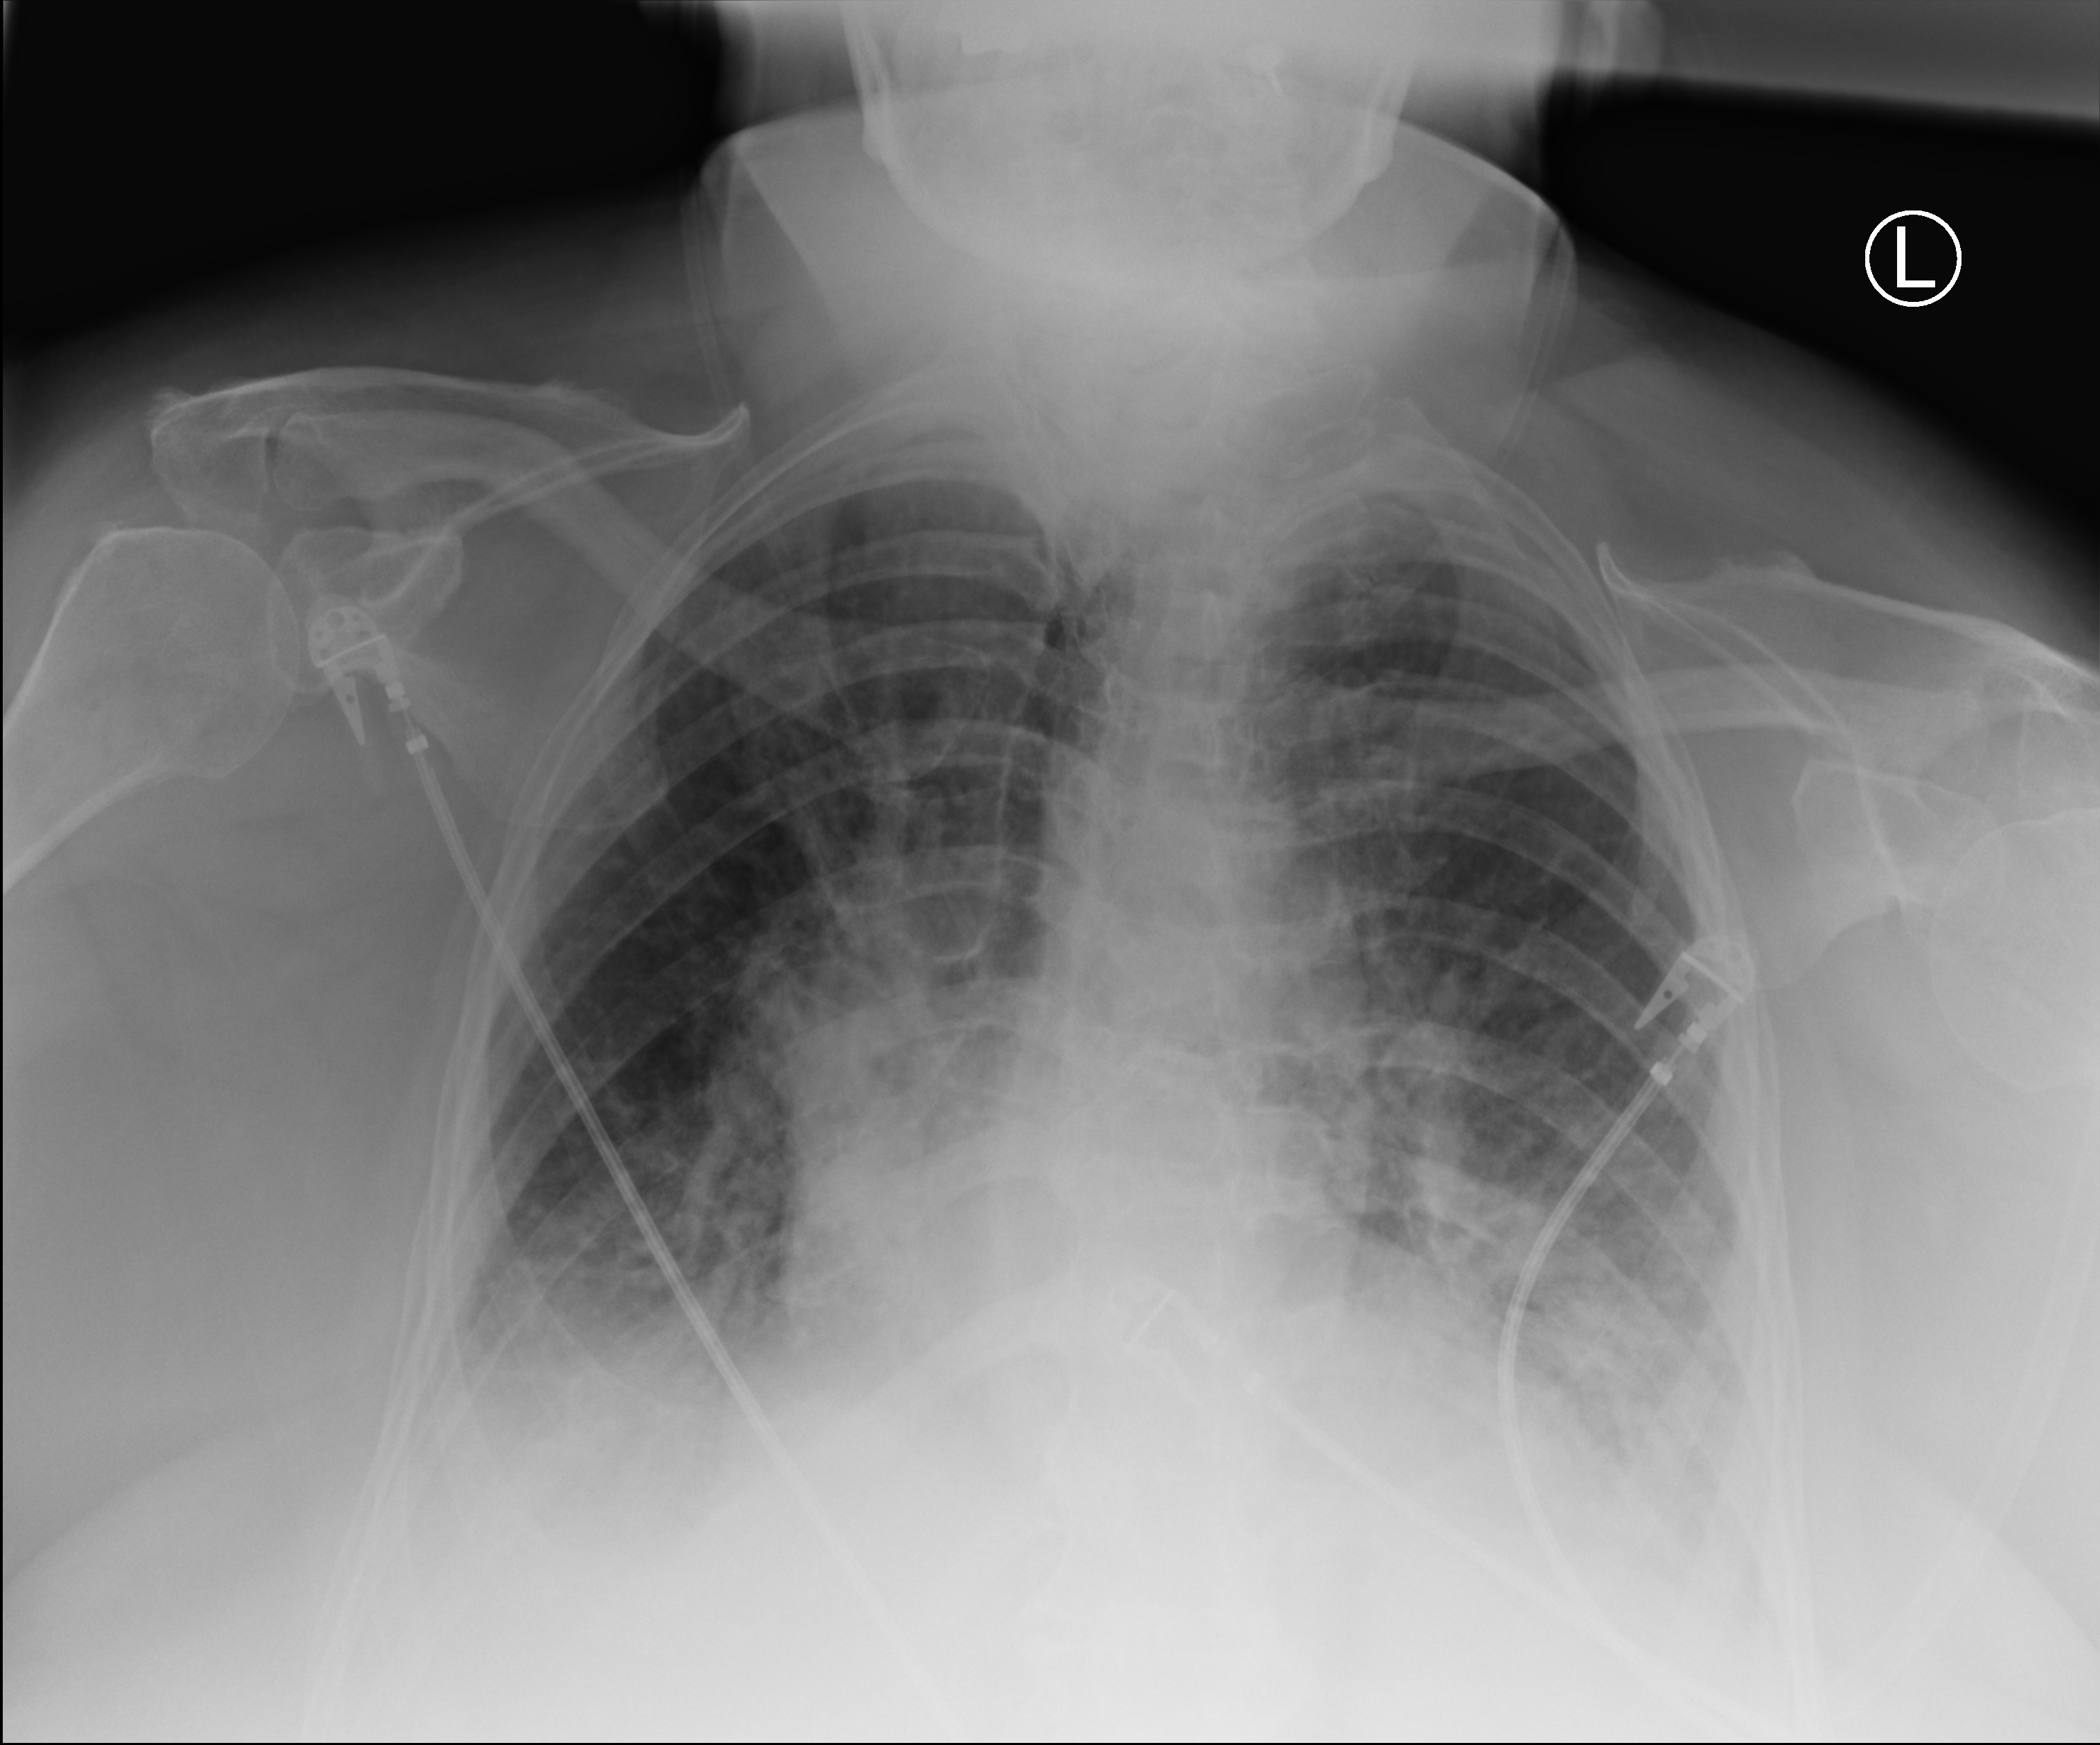
Portable chest radiograph; anteroposterior (AP) projection. Female patient hospitalised with COVID-19, age 75–90 years.
Admission-level facts for this patient (not findings on this image; timing relative to this image not recorded): other chronic lung disease (admission record): yes; admitted to intensive care during this hospital stay: no.